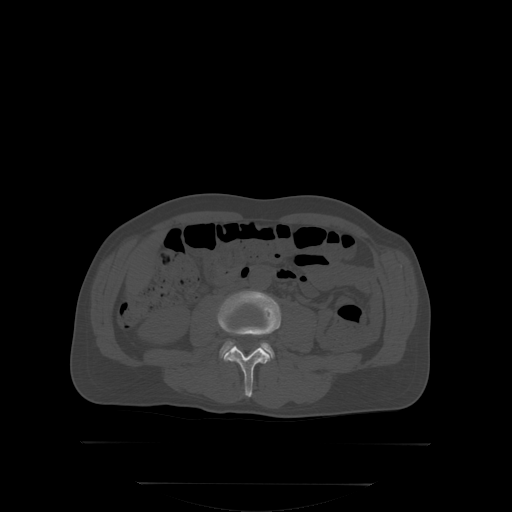
CT including the spine, one axial slice. Position 118 of 350 along the scan axis. Bone window (W 1800 / L 400 HU). 2.5 mm slice thickness. 512 × 512 image matrix, field of view 500 × 500 mm. Patient: male, 58 years. From the clinical record (not read from this slice): primary cancer: prostate; vertebrae with lytic lesions (as recorded): L1.
Annotated regions visible in this slice (semi-automatically segmented with operator editing):
- L3 vertebra: bounding box <219,292,280,396> (left, top, right, bottom; pixels)
- L4 vertebra: <219,340,275,359>